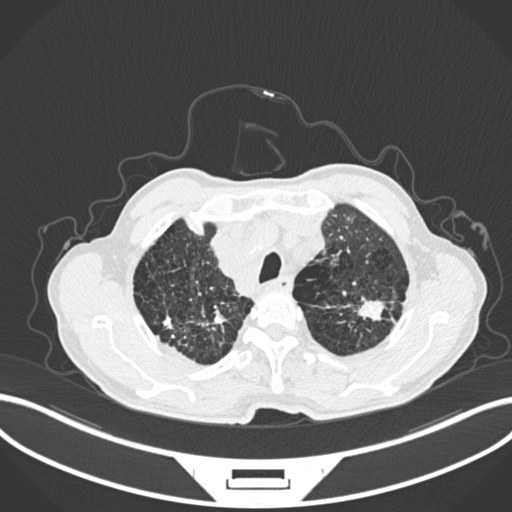
Chest CT, one axial slice. Position 233 of 287 along the scan axis. Reconstruction kernel B30f. 120 kVp. Lung window (W 1500 / L -600 HU). 1 mm slice thickness. 512 × 512 image matrix, field of view 400 × 400 mm. Male patient, age 74 years. From the clinical record (not read from this slice): clinical TNM (as recorded): T2a N1 M0.
Structures marked on this image (rectangle marked by the reading radiologist):
- lung tumour (recorded histology: adenocarcinoma): bounding box (x1, y1, x2, y2) in pixels: (350, 296, 390, 325)